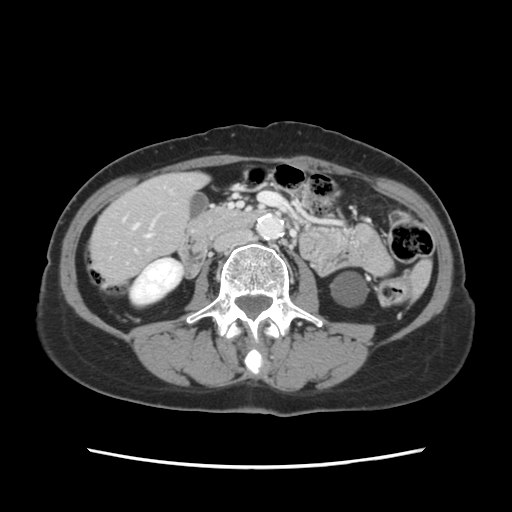
Contrast-enhanced abdominal CT, one axial slice; position 24 of 120 along the scan axis; 120 kVp; soft-tissue window (W 400 / L 40 HU); 2.5 mm slice thickness; 512 × 512 image matrix, field of view 330 × 330 mm. Female patient, age 70 years. Case-level facts recorded for this patient, not image findings: diagnosis: colorectal cancer liver metastases, imaged before liver resection; multiple liver metastases: no; largest metastasis: 2.5 cm.
Outlined on this slice (manually delineated by an expert):
- hepatic veins: bounding box (x1, y1, x2, y2) in pixels: (147, 234, 151, 237)
- liver: (93, 174, 204, 279)
- planned liver remnant (the part of the liver to remain after resection): (92, 175, 204, 279)
- portal vein (with intrahepatic branches): (132, 224, 139, 230)